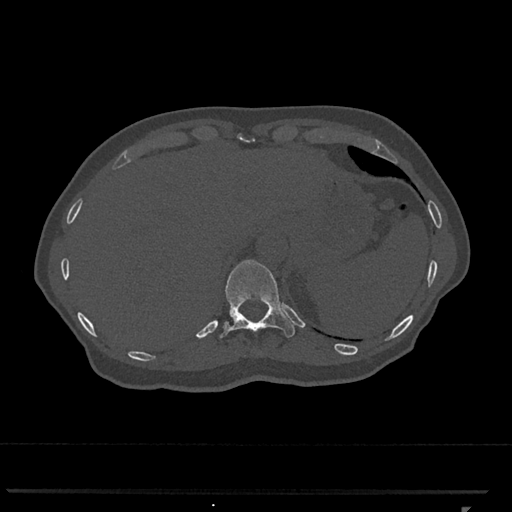
CT including the spine, one axial slice. Slice 522 of 793 in the series (ordered by position). Reconstruction kernel Br40s/3. Bone window (W 1800 / L 400 HU). 0.5 mm slice thickness. 512 × 512 image matrix, field of view 380 × 380 mm. Female patient, age 62 years. Case-level facts recorded for this patient, not image findings: primary cancer: renal.
Annotated regions visible in this slice (semi-automatic segmentation, software-assisted and operator-edited):
- T11 vertebra: bounding box <219,259,295,338> (left, top, right, bottom; pixels)